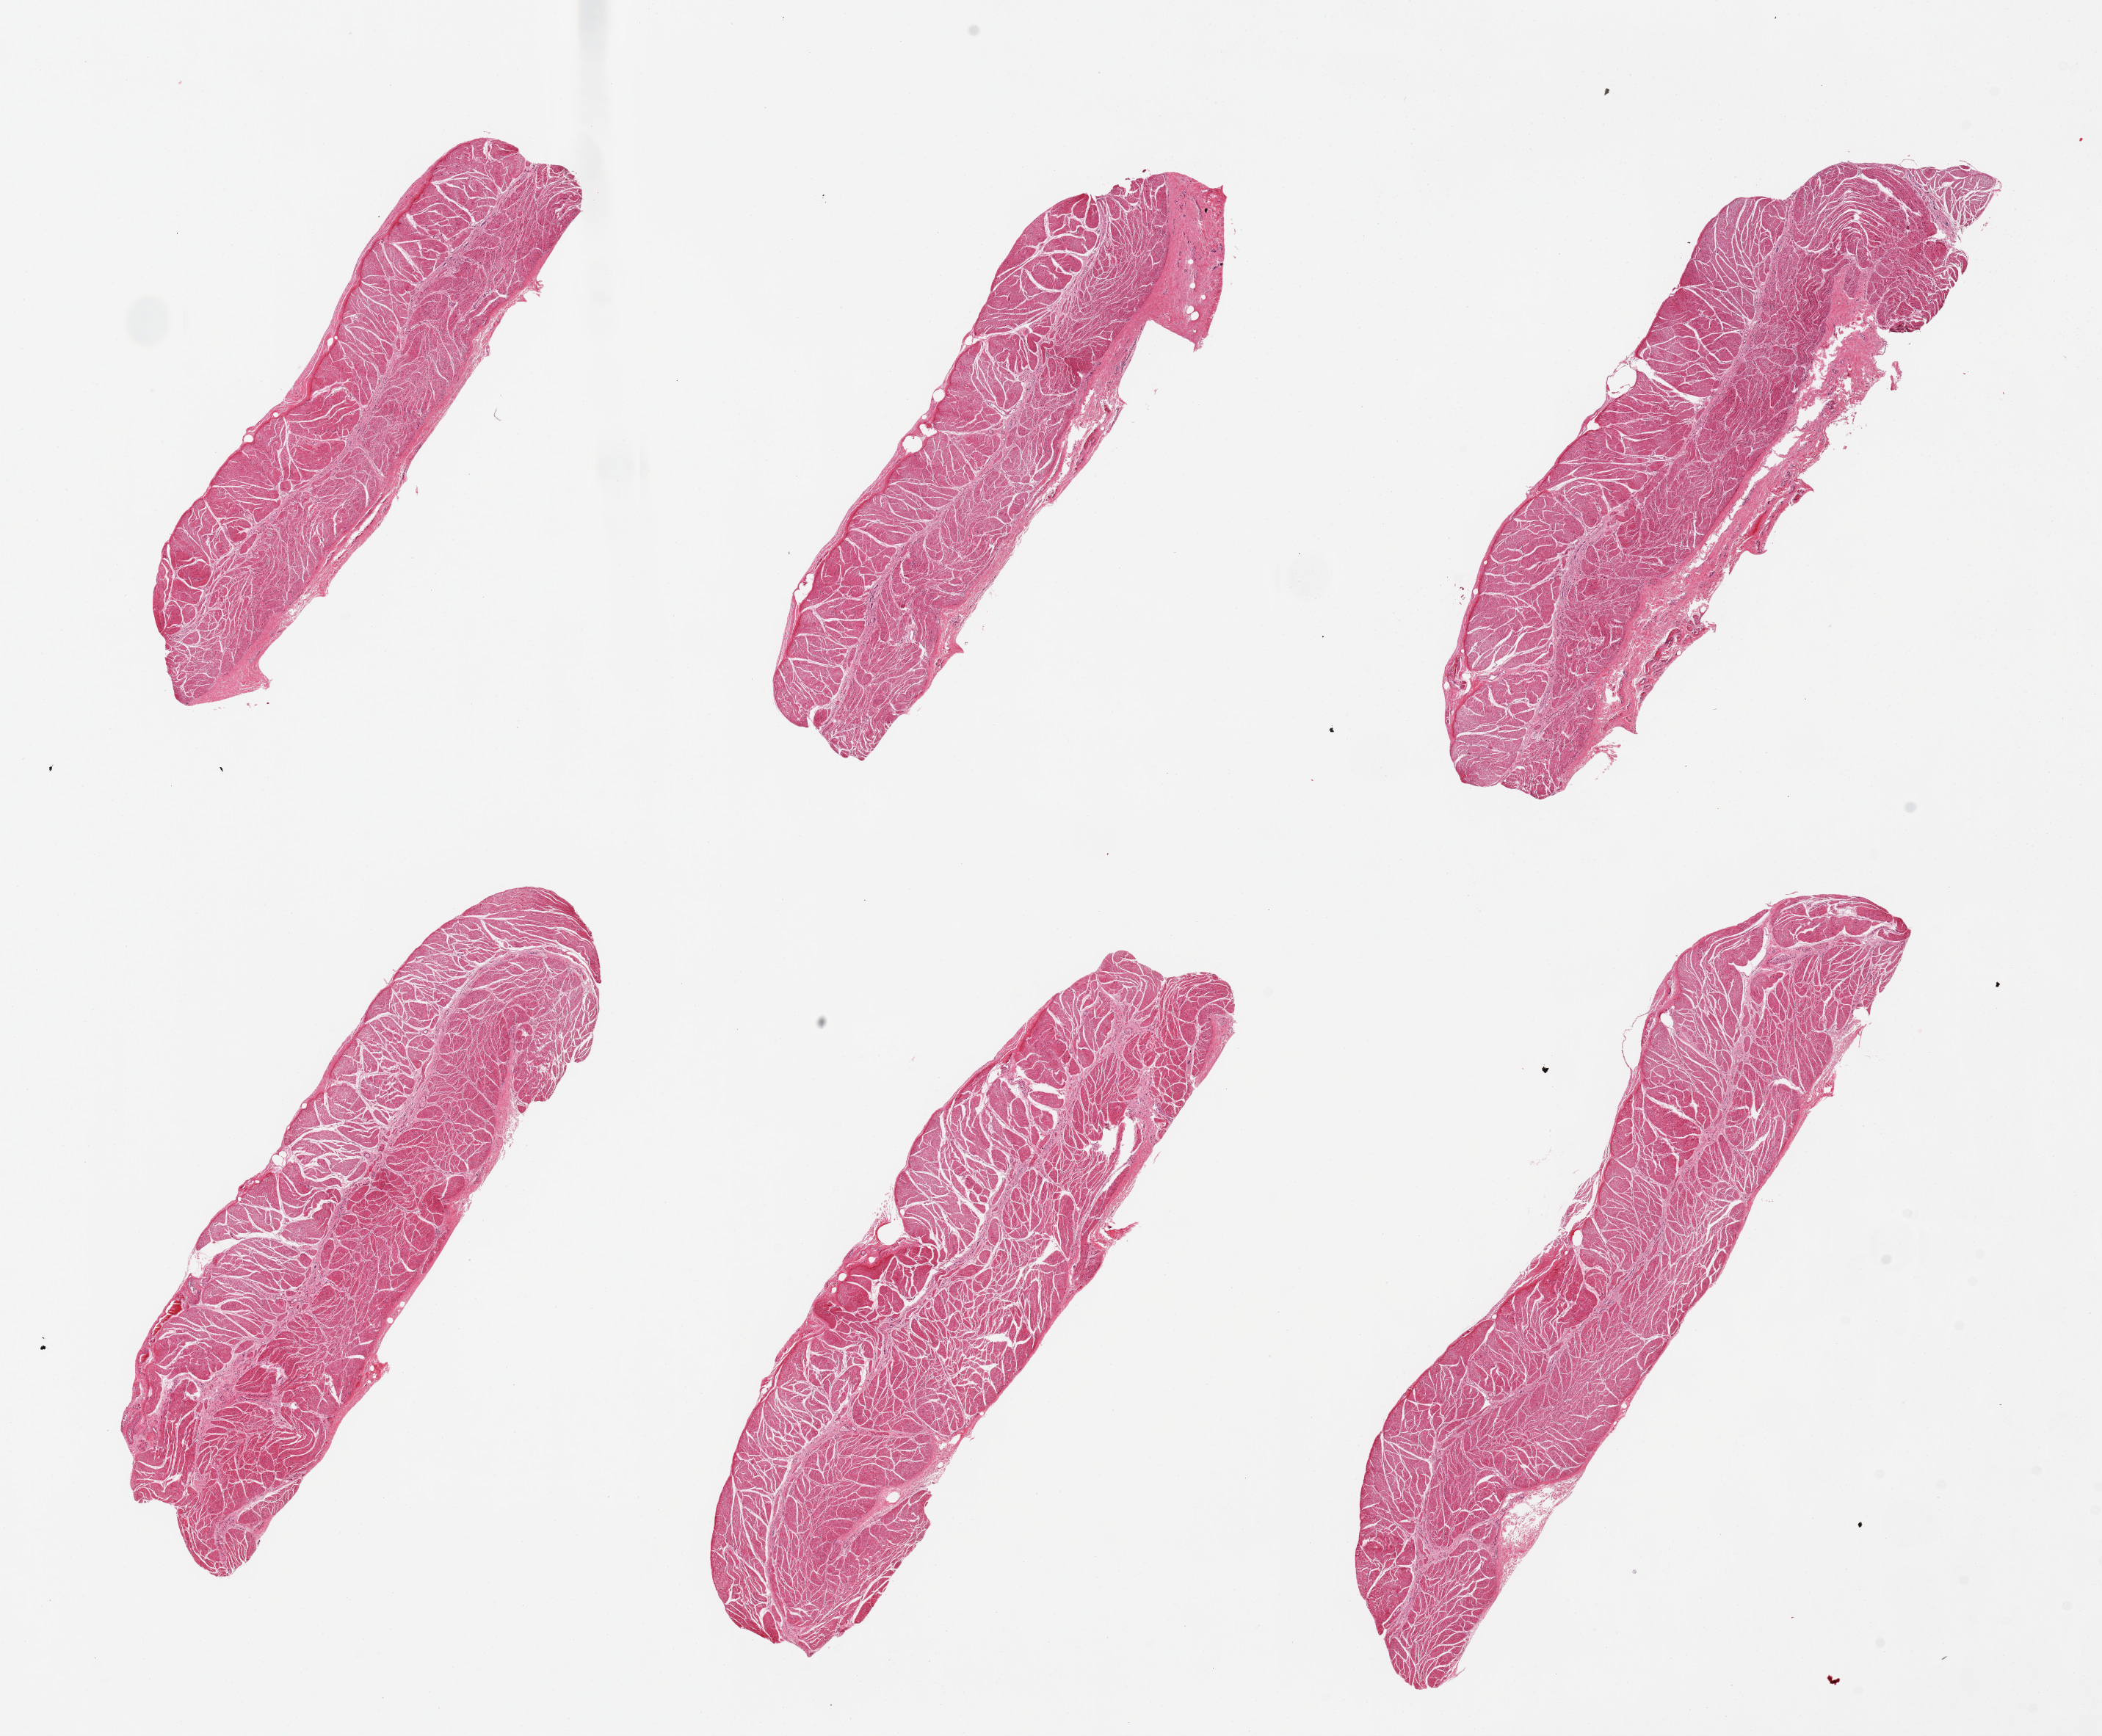
Digitized hematoxylin and eosin (H&E)-stained section — a low-resolution overview of the entire scanned area, about 22.6 x 18.7 mm, PAXgene-fixed paraffin-embedded (PFPE) section, sampled site (target tissue): esophageal muscle, donor tissue sample. Donor: female.
• reviewer comment on this tissue sample: 6 pieces, all muscularis, excellent specimens